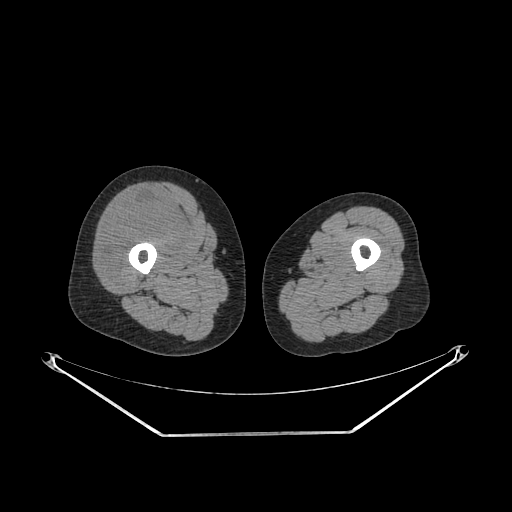
CT of an extremity soft-tissue mass (from a PET/CT study), one axial slice; position 234 of 311 along the scan axis; 140 kVp; soft-tissue window (W 400 / L 40 HU); 3.75 mm slice thickness; 512 × 512 image matrix, field of view 500 × 500 mm. Female patient. From the clinical record (not read from this slice): histological type: pleiomorphic undifferentiated sarcoma; grade: high; site of the primary tumour: right quadricep.
Structures marked on this image (expert contour drawn on MRI and transferred to this co-registered scan by the dataset authors):
- tumour plus oedema (research contour): bounding box (x1, y1, x2, y2) in pixels: (100, 199, 184, 282)
- tumour (research contour): (100, 199, 184, 282)